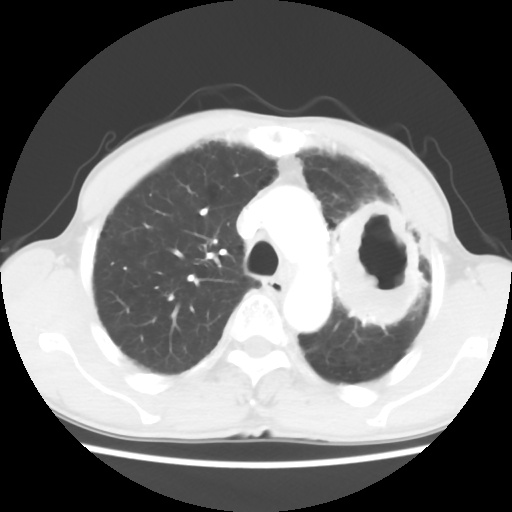
Chest CT, one axial slice. Slice 43 of 60 in the series (ordered by position). Lung window (W 1500 / L -600 HU). 5 mm slice thickness. 512 × 512 image matrix, field of view 308 × 308 mm. Patient: male, 64 years. Case-level facts recorded for this patient, not image findings: clinical TNM (as recorded): T3 N3 M0.
Structures marked on this image (rectangle marked by the reading radiologist):
- lung tumour (recorded histology: adenocarcinoma): bounding box (x1, y1, x2, y2) in pixels: (320, 192, 428, 336)